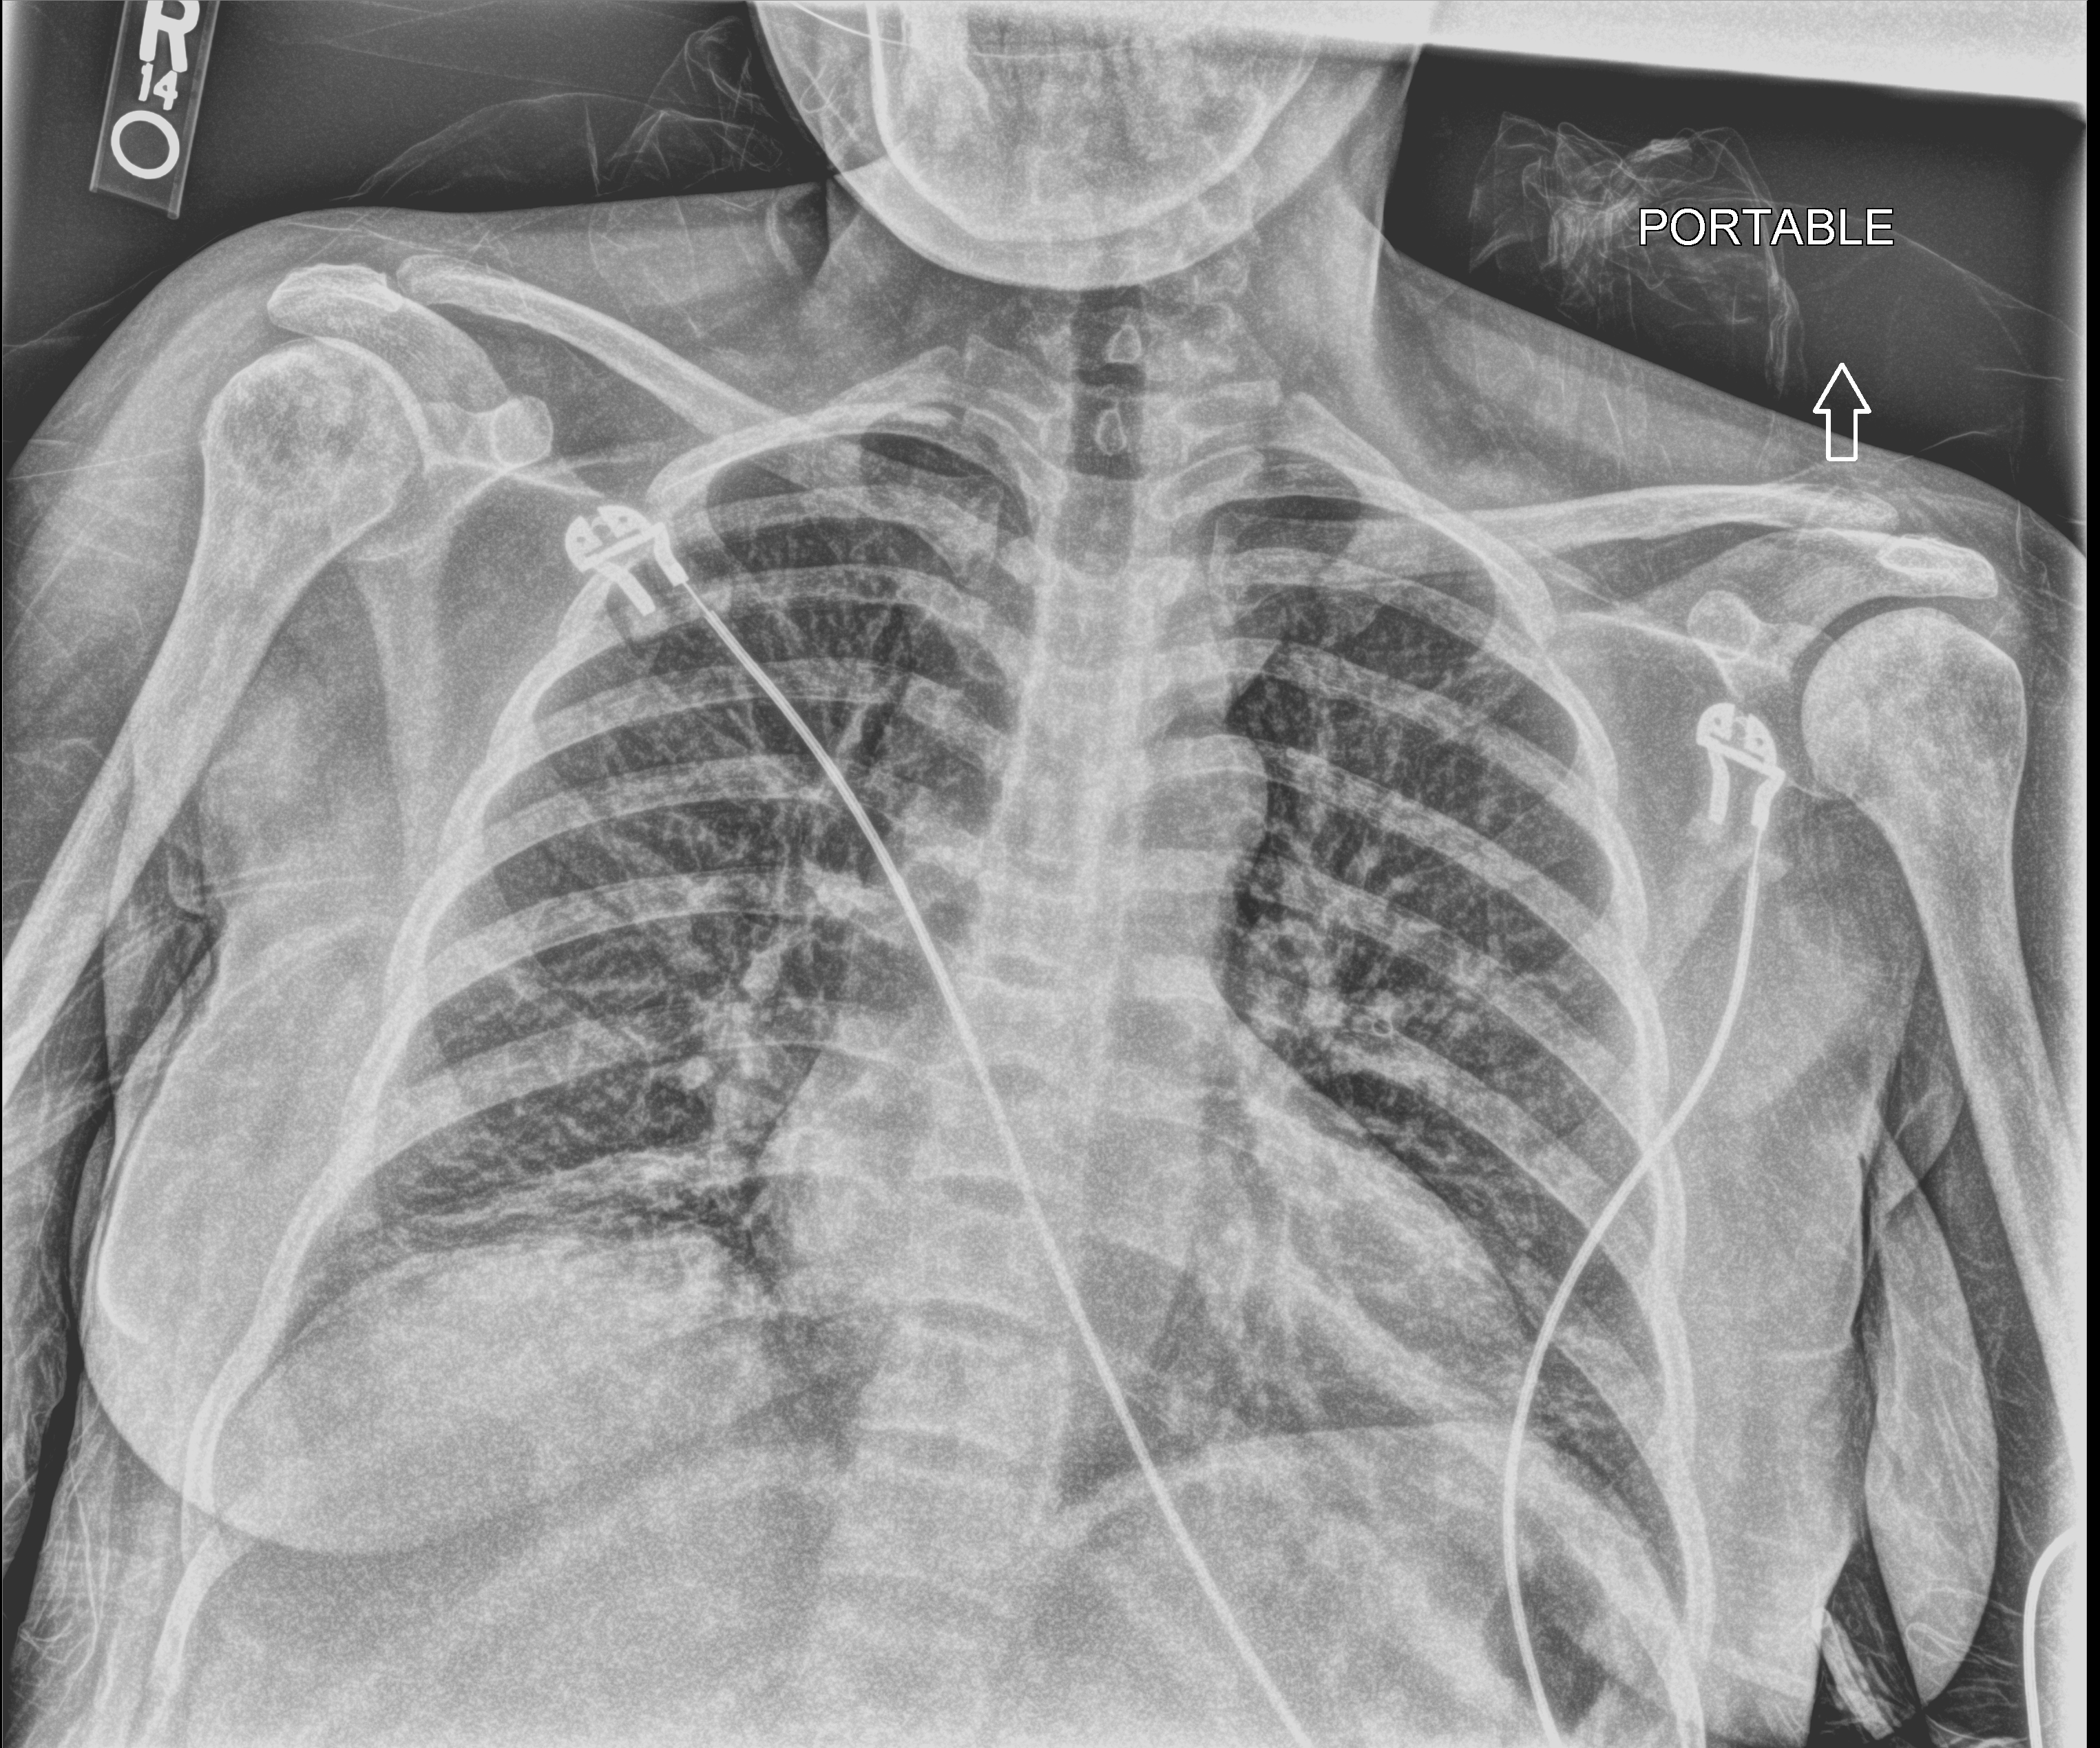
Chest X-ray (portable). Patient hospitalised with COVID-19; female, aged 18–59 years.
From the hospital-stay record, not from the radiograph (when in the stay this image was taken is not recorded):
- length of hospital stay: 9 days
- mechanically ventilated during this hospital stay: no
- admitted to intensive care during this hospital stay: no